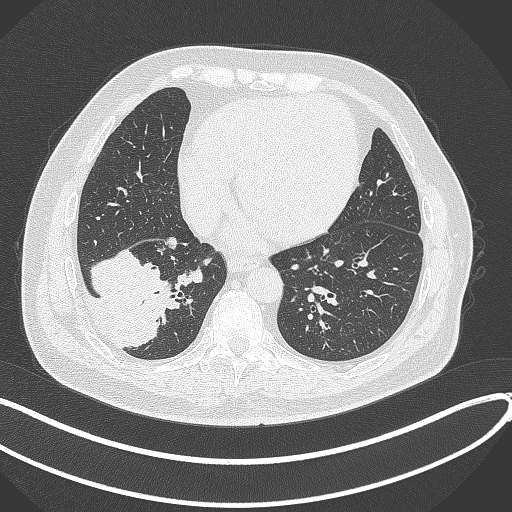
Chest CT, one axial slice; position 118 of 360 along the scan axis; reconstruction kernel B70f; lung window (W 1500 / L -600 HU); 1 mm slice thickness; 512 × 512 image matrix. Male patient, age 59 years.
Structures marked on this image (rectangle marked by the reading radiologist):
- lung tumour (recorded histology: adenocarcinoma): bounding box <88,250,181,353> (left, top, right, bottom; pixels)